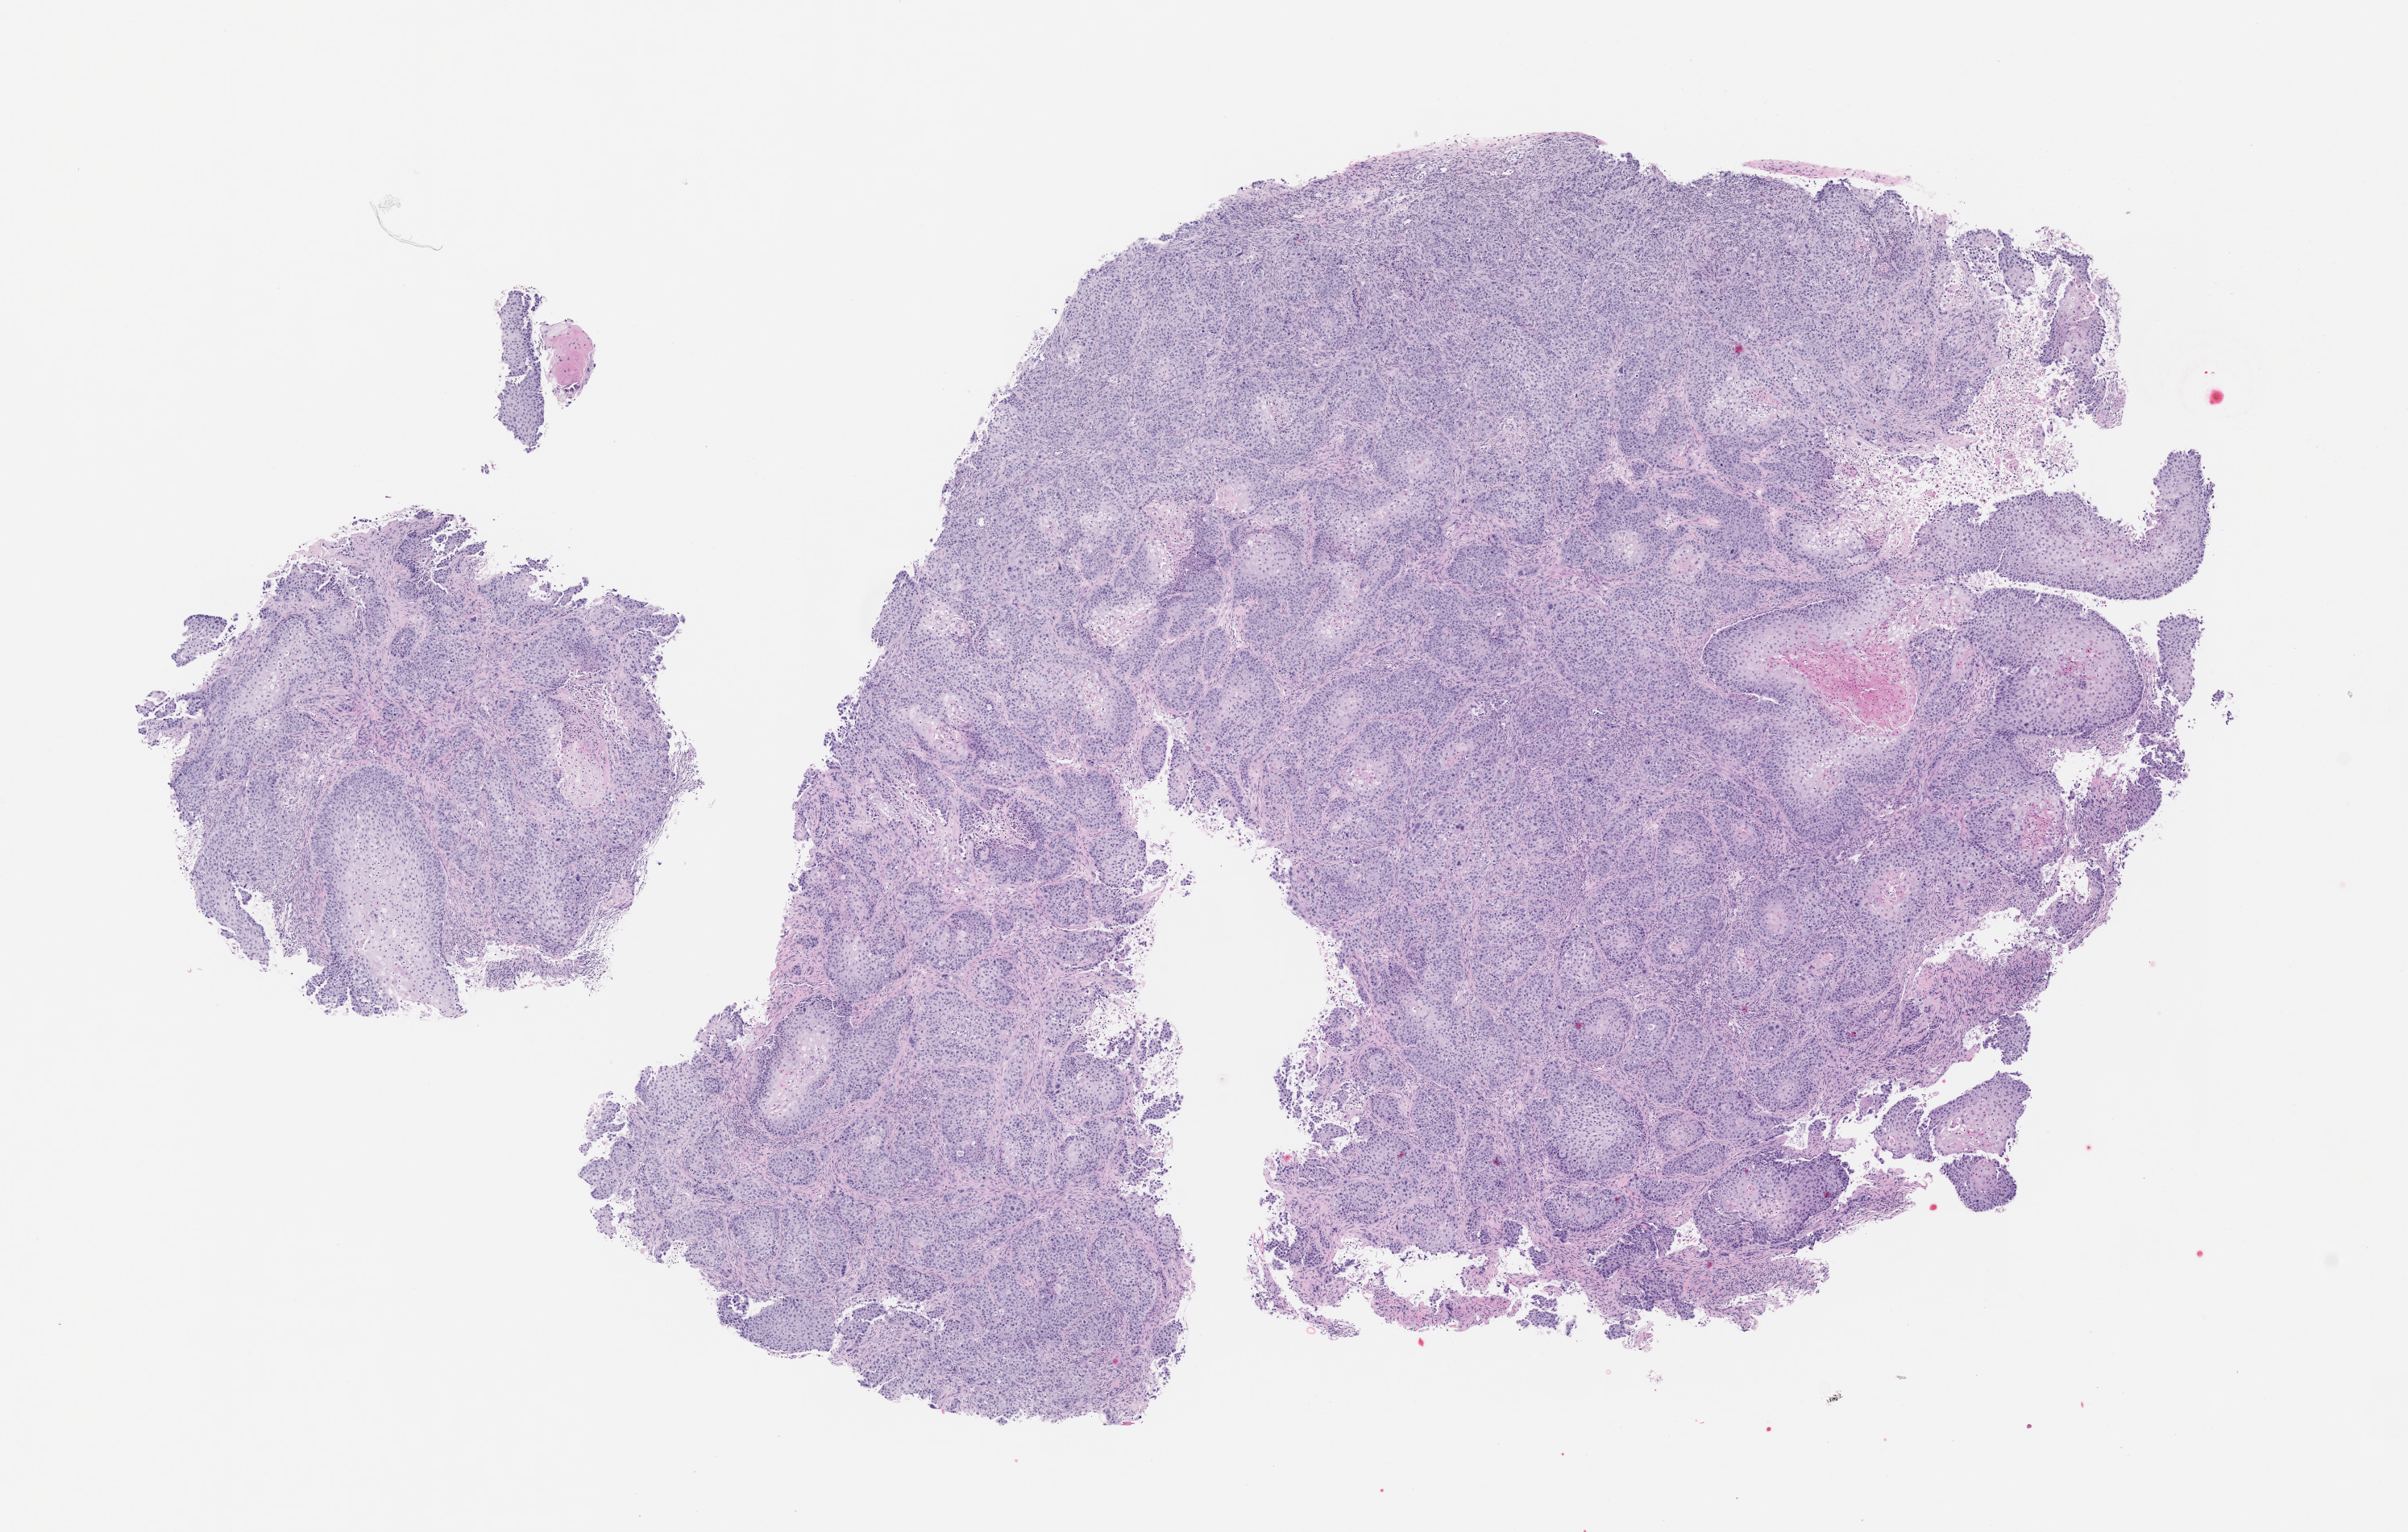
Whole-slide image, hematoxylin and eosin (H&E): patient-derived xenograft (human tumor grown in a mouse), passage 1, shown as a low-resolution overview of the whole scanned area (about 12.0 x 7.6 mm). Formalin-fixed paraffin-embedded section. Tumor site category: lung.
Originating patient diagnosis: Lung Squamous Cell Carcinoma.